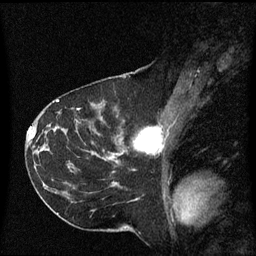
Breast MRI (dynamic contrast-enhanced), one sagittal slice; position 34 of 60 along the scan axis; dynamic contrast-enhanced series, image 2 of 3 at this slice position (ordered by acquisition); 1.5 T; TE 4.2 ms, TR 8.4 ms; 2 mm slice thickness; 256 × 256 image matrix, field of view 220 × 220 mm. Patient: female, 41 years. Case-level facts recorded for this patient, not image findings: setting: breast cancer imaged before/during neoadjuvant chemotherapy; receptor status: triple-negative.
Outlined on this slice (semi-automatic segmentation, software-assisted and operator-edited):
- analysis volume of interest (the breast-tissue region the enhancement analysis was run in; not a lesion): bounding box (x1, y1, x2, y2) in pixels: (116, 116, 165, 163)
- tumour enhancement mask (voxels above the 70 % enhancement threshold inside the analysis volume of interest): (135, 128, 162, 153)